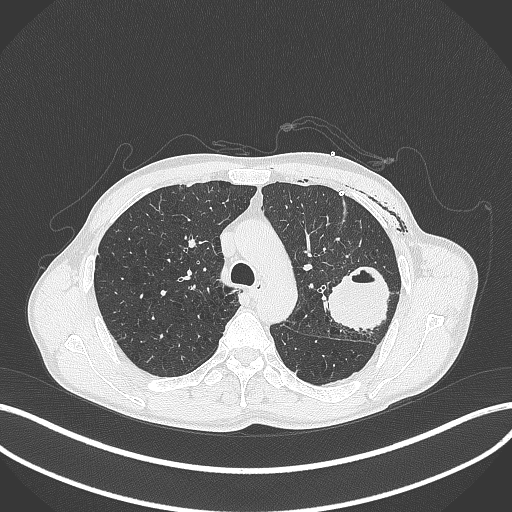
Chest CT, one axial slice; slice 285 of 457 in the series (ordered by position); reconstruction kernel B70f; 120 kVp; lung window (W 1500 / L -600 HU); 1 mm slice thickness; 512 × 512 image matrix, field of view 400 × 400 mm. Male patient, age 58 years. Case-level facts recorded for this patient, not image findings: clinical TNM (as recorded): T3 N0 M0.
Annotated regions visible in this slice (bounding box drawn by a radiologist):
- lung tumour (recorded histology: adenocarcinoma): bounding box (x1, y1, x2, y2) in pixels: (324, 262, 392, 335)